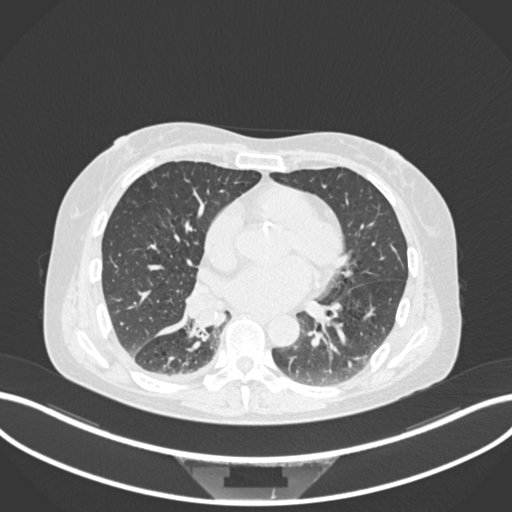
Chest CT, one axial slice; 120 kVp; lung window (W 1500 / L -600 HU); 512 × 512 image matrix, field of view 400 × 400 mm. Patient: female, 63 years. Case-level facts recorded for this patient, not image findings: clinical TNM (as recorded): T1c N0 M0.
Structures marked on this image (bounding box drawn by a radiologist):
- lung tumour (recorded histology: adenocarcinoma): bounding box (x1, y1, x2, y2) in pixels: (184, 282, 235, 347)